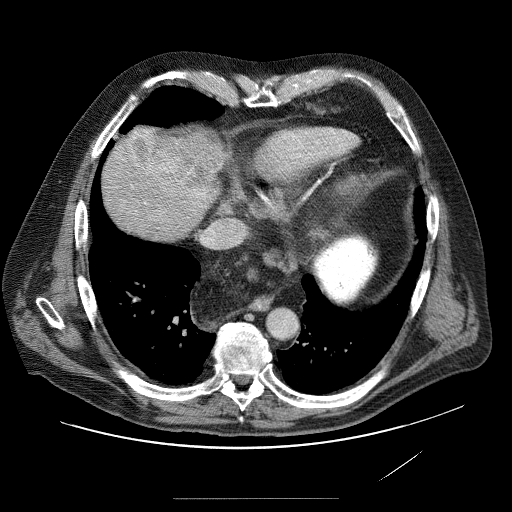
Contrast-enhanced abdominal CT (liver protocol), one axial slice; position 76 of 89 along the scan axis; soft-tissue window (W 400 / L 40 HU); 2.5 mm slice thickness; 512 × 512 image matrix, field of view 420 × 420 mm. From the clinical record (not read from this slice): diagnosis: hepatocellular carcinoma (patient treated with transarterial chemoembolisation; whether this scan precedes or follows treatment is not stated here); TNM stage (as recorded): Stage-IVA; Child-Pugh class: A; tumour nodularity: multinodular.
Outlined on this slice (semi-automatically segmented with operator editing):
- liver parenchyma outside the tumour (the mass and vessels are separate outlines, so this box may not span the whole liver): bounding box (x1, y1, x2, y2) in pixels: (108, 132, 214, 226)
- mass: (132, 131, 220, 219)
- liver vessels: (132, 155, 165, 200)